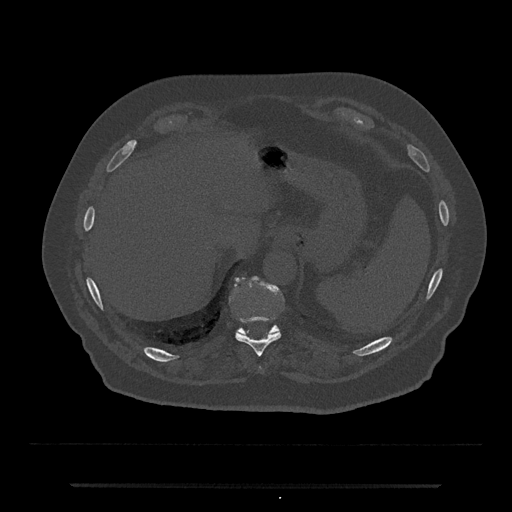
CT including the spine, one axial slice. Position 690 of 797 along the scan axis. Reconstruction kernel Br40s/3. 120 kVp. Bone window (W 1800 / L 400 HU). 0.5 mm slice thickness. 512 × 512 image matrix, field of view 434 × 434 mm. Male patient, age 80 years. Case-level facts recorded for this patient, not image findings: primary cancer: prostate.
Annotated regions visible in this slice (semi-automatically segmented with operator editing):
- T10 vertebra: bounding box (x1, y1, x2, y2) in pixels: (235, 278, 281, 357)
- T11 vertebra: (235, 276, 281, 334)